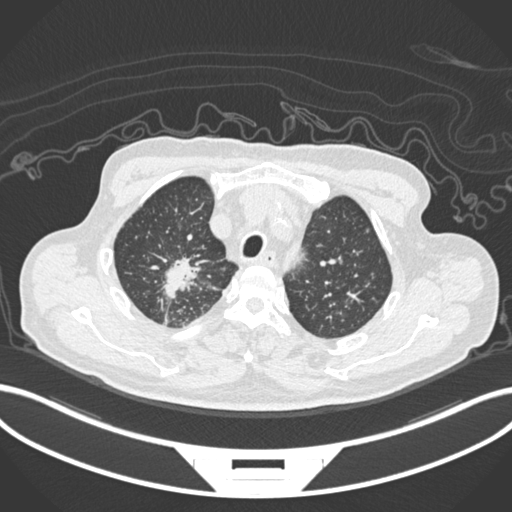
Chest CT, one axial slice. Position 174 of 207 along the scan axis. 120 kVp. Lung window (W 1500 / L -600 HU). 512 × 512 image matrix, field of view 400 × 400 mm. Patient: male, 69 years. From the clinical record (not read from this slice): clinical TNM (as recorded): T1c N1 M1.
Structures marked on this image (rectangle marked by the reading radiologist):
- lung tumour (recorded histology: adenocarcinoma): box from (x=160, y=251) to (x=209, y=303) px